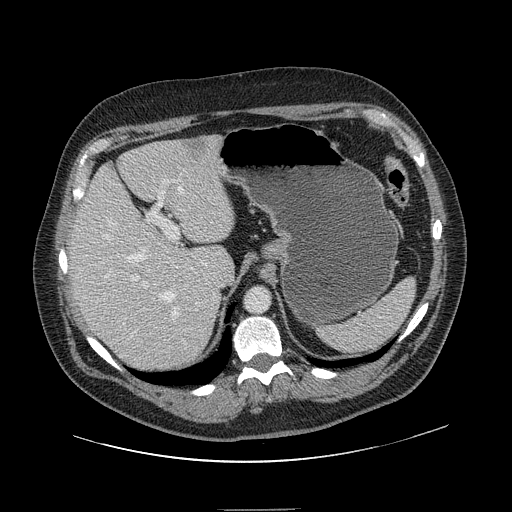
Contrast-enhanced abdominal CT, one axial slice; slice 106 of 154 in the series (ordered by position); 120 kVp; intravenous contrast given; soft-tissue window (W 400 / L 40 HU); 2.5 mm slice thickness; 512 × 512 image matrix, field of view 451 × 451 mm. Male patient, age 61 years. Case-level facts recorded for this patient, not image findings: diagnosis: colorectal cancer liver metastases, imaged before liver resection; multiple liver metastases: yes; largest metastasis: 2.6 cm; chemotherapy before resection: no.
Structures marked on this image (expert manual segmentation):
- hepatic veins: bounding box <104,186,183,318> (left, top, right, bottom; pixels)
- liver: <69,137,235,373>
- planned liver remnant (the part of the liver to remain after resection): <69,144,235,360>
- portal vein (with intrahepatic branches): <133,179,184,287>
- liver metastasis: <184,141,208,162>